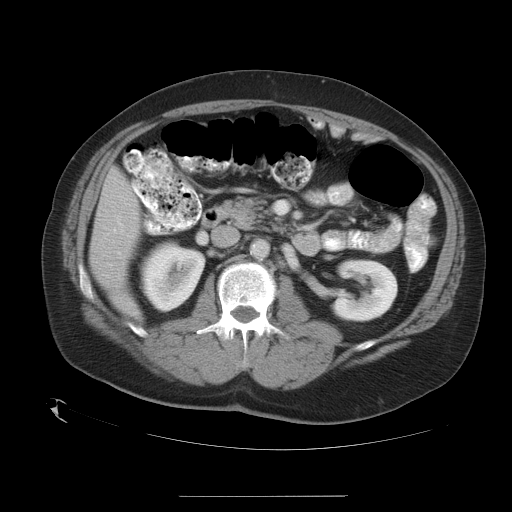
Contrast-enhanced abdominal CT, one axial slice. Slice 12 of 35 in the series (ordered by position). Reconstruction kernel STANDARD. Intravenous contrast given. Soft-tissue window (W 400 / L 40 HU). 512 × 512 image matrix, field of view 450 × 450 mm. Male patient, age 67 years. Case-level facts recorded for this patient, not image findings: diagnosis: colorectal cancer liver metastases, imaged before liver resection; multiple liver metastases: no.
Annotated regions visible in this slice (outlined manually by an expert reader):
- liver: bounding box [x1, y1, x2, y2] px = [91, 172, 140, 313]
- planned liver remnant (the part of the liver to remain after resection): [91, 172, 140, 312]
- portal vein (with intrahepatic branches): [114, 186, 136, 233]